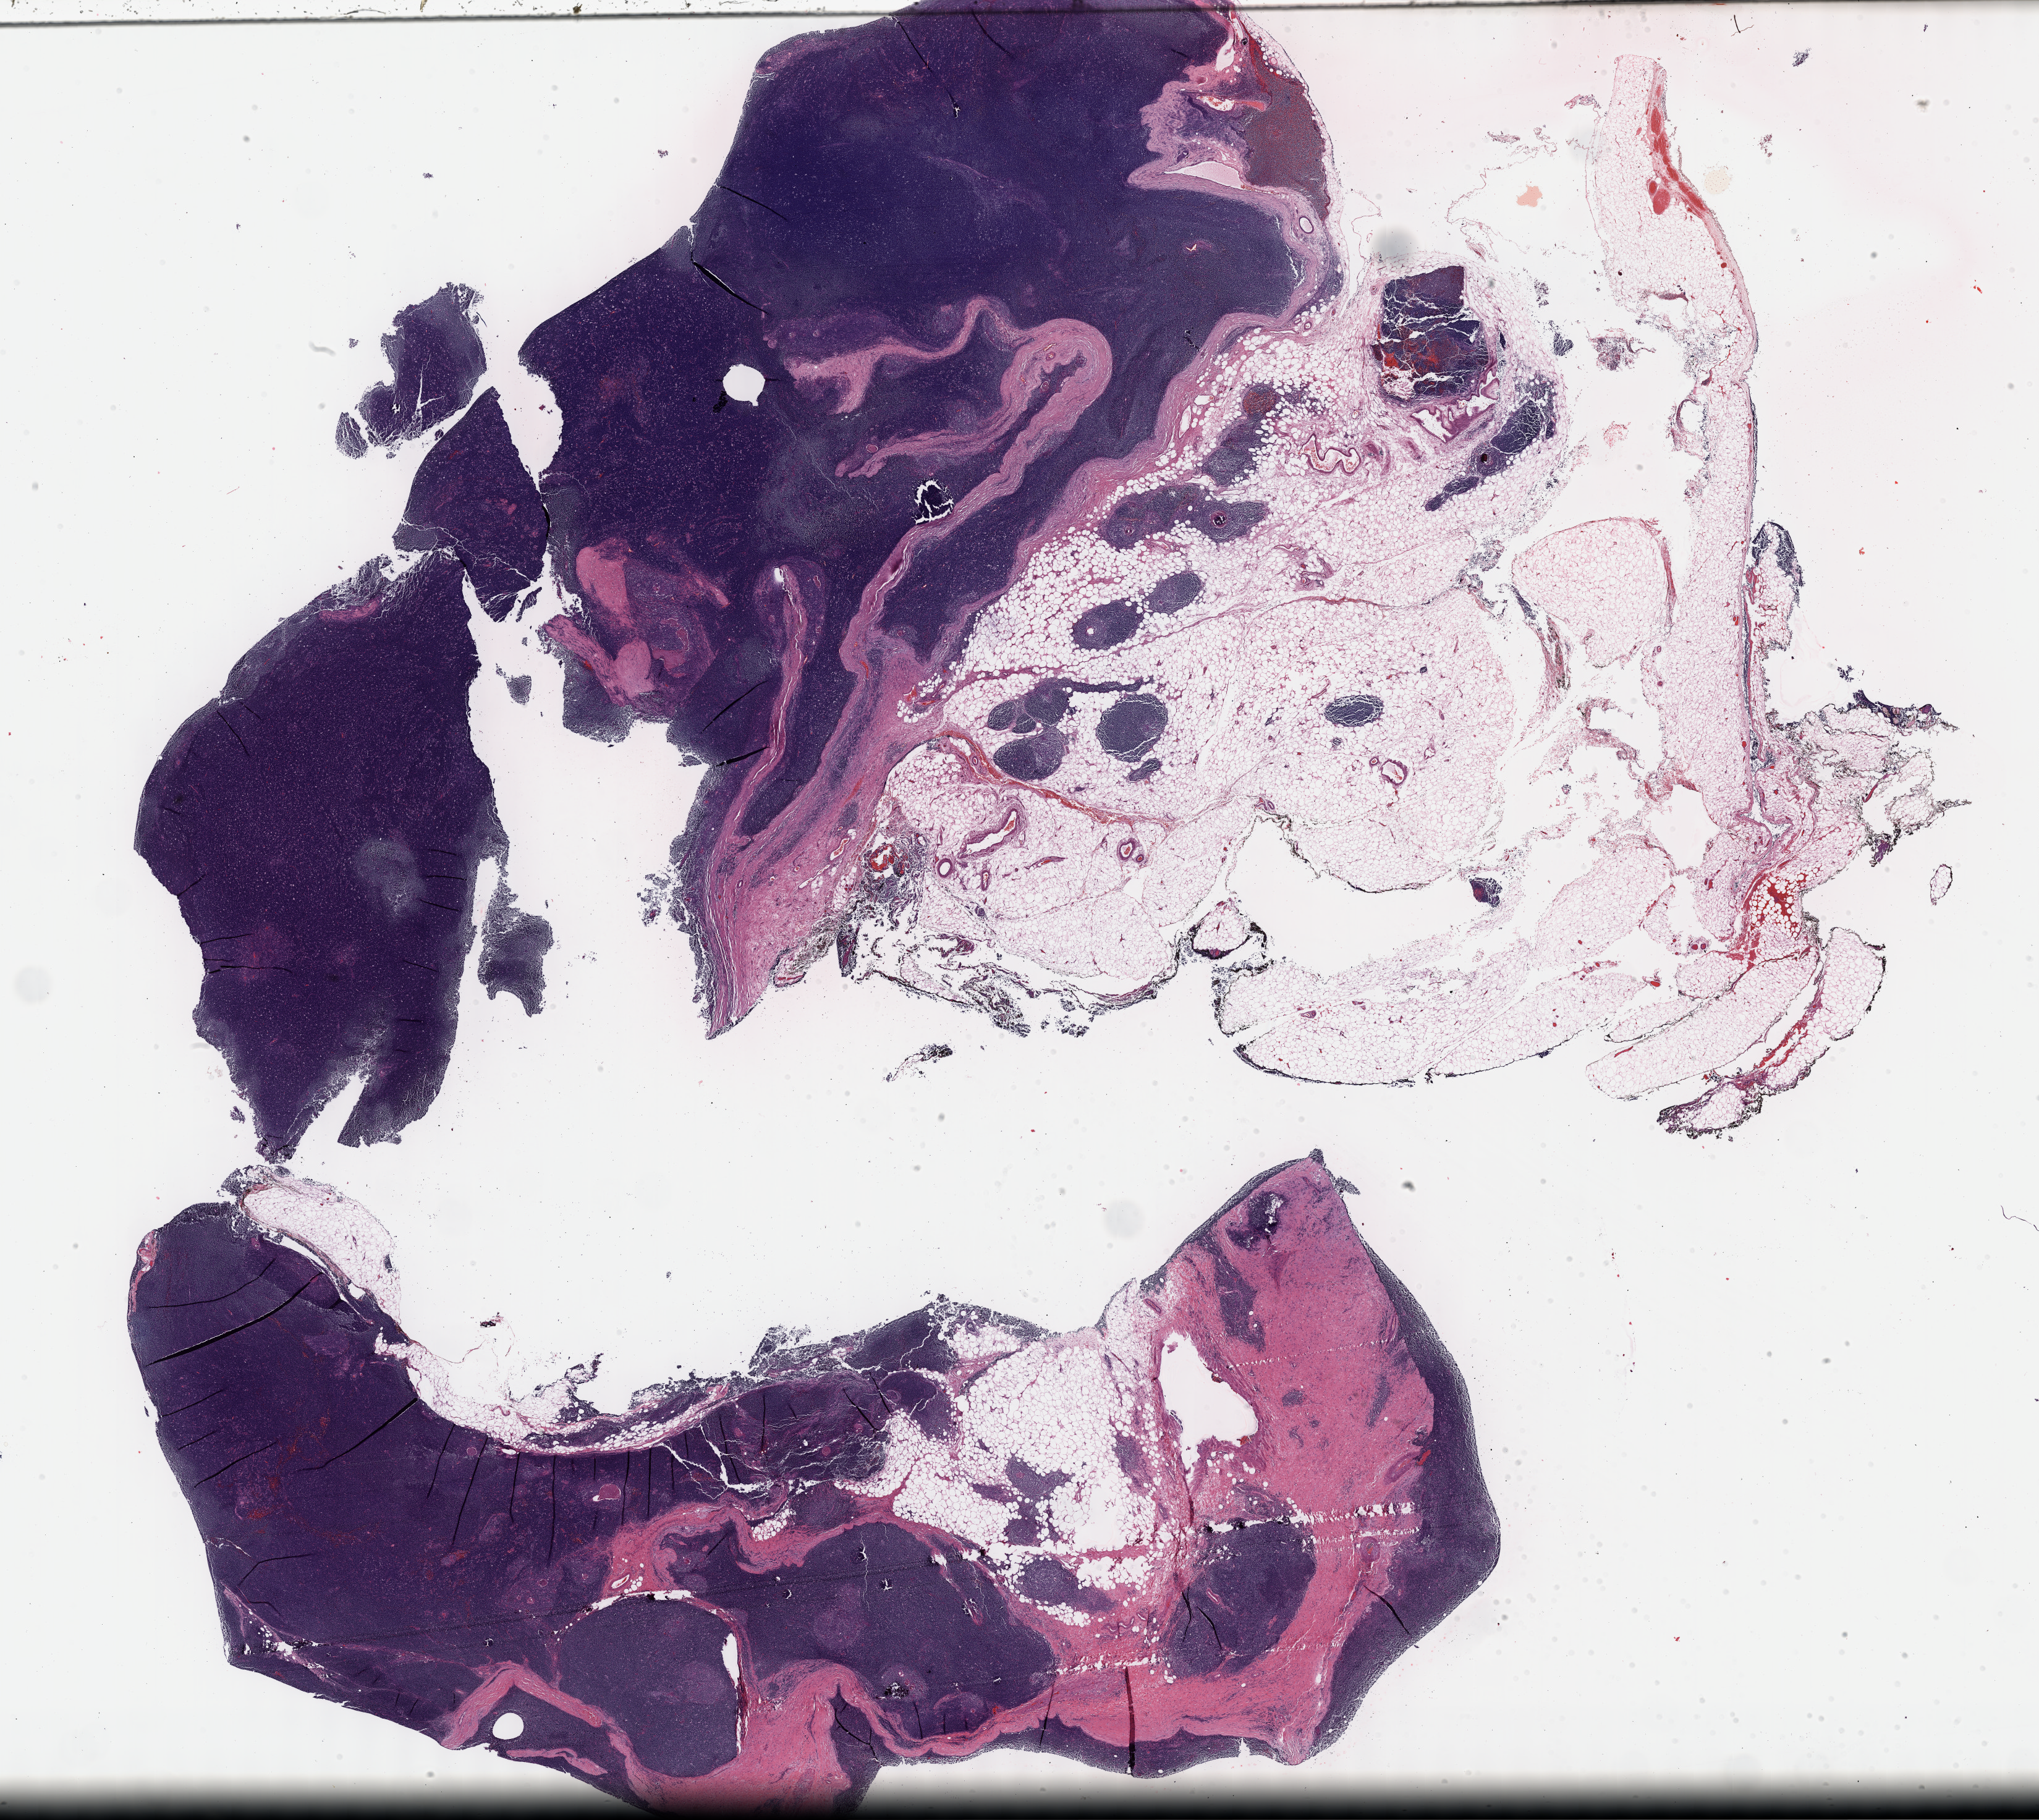
Whole-slide histology image, Hematoxylin and eosin (H&E) stained, a low-resolution overview of the entire scanned area, about 26.7 x 23.8 mm (acquisition: 40x scan), formalin-fixed paraffin-embedded (FFPE) diagnostic section, sample: primary tumour, thymus. Male, age 44 years at initial diagnosis.
* histologic diagnosis: Thymoma, type B1, malignant